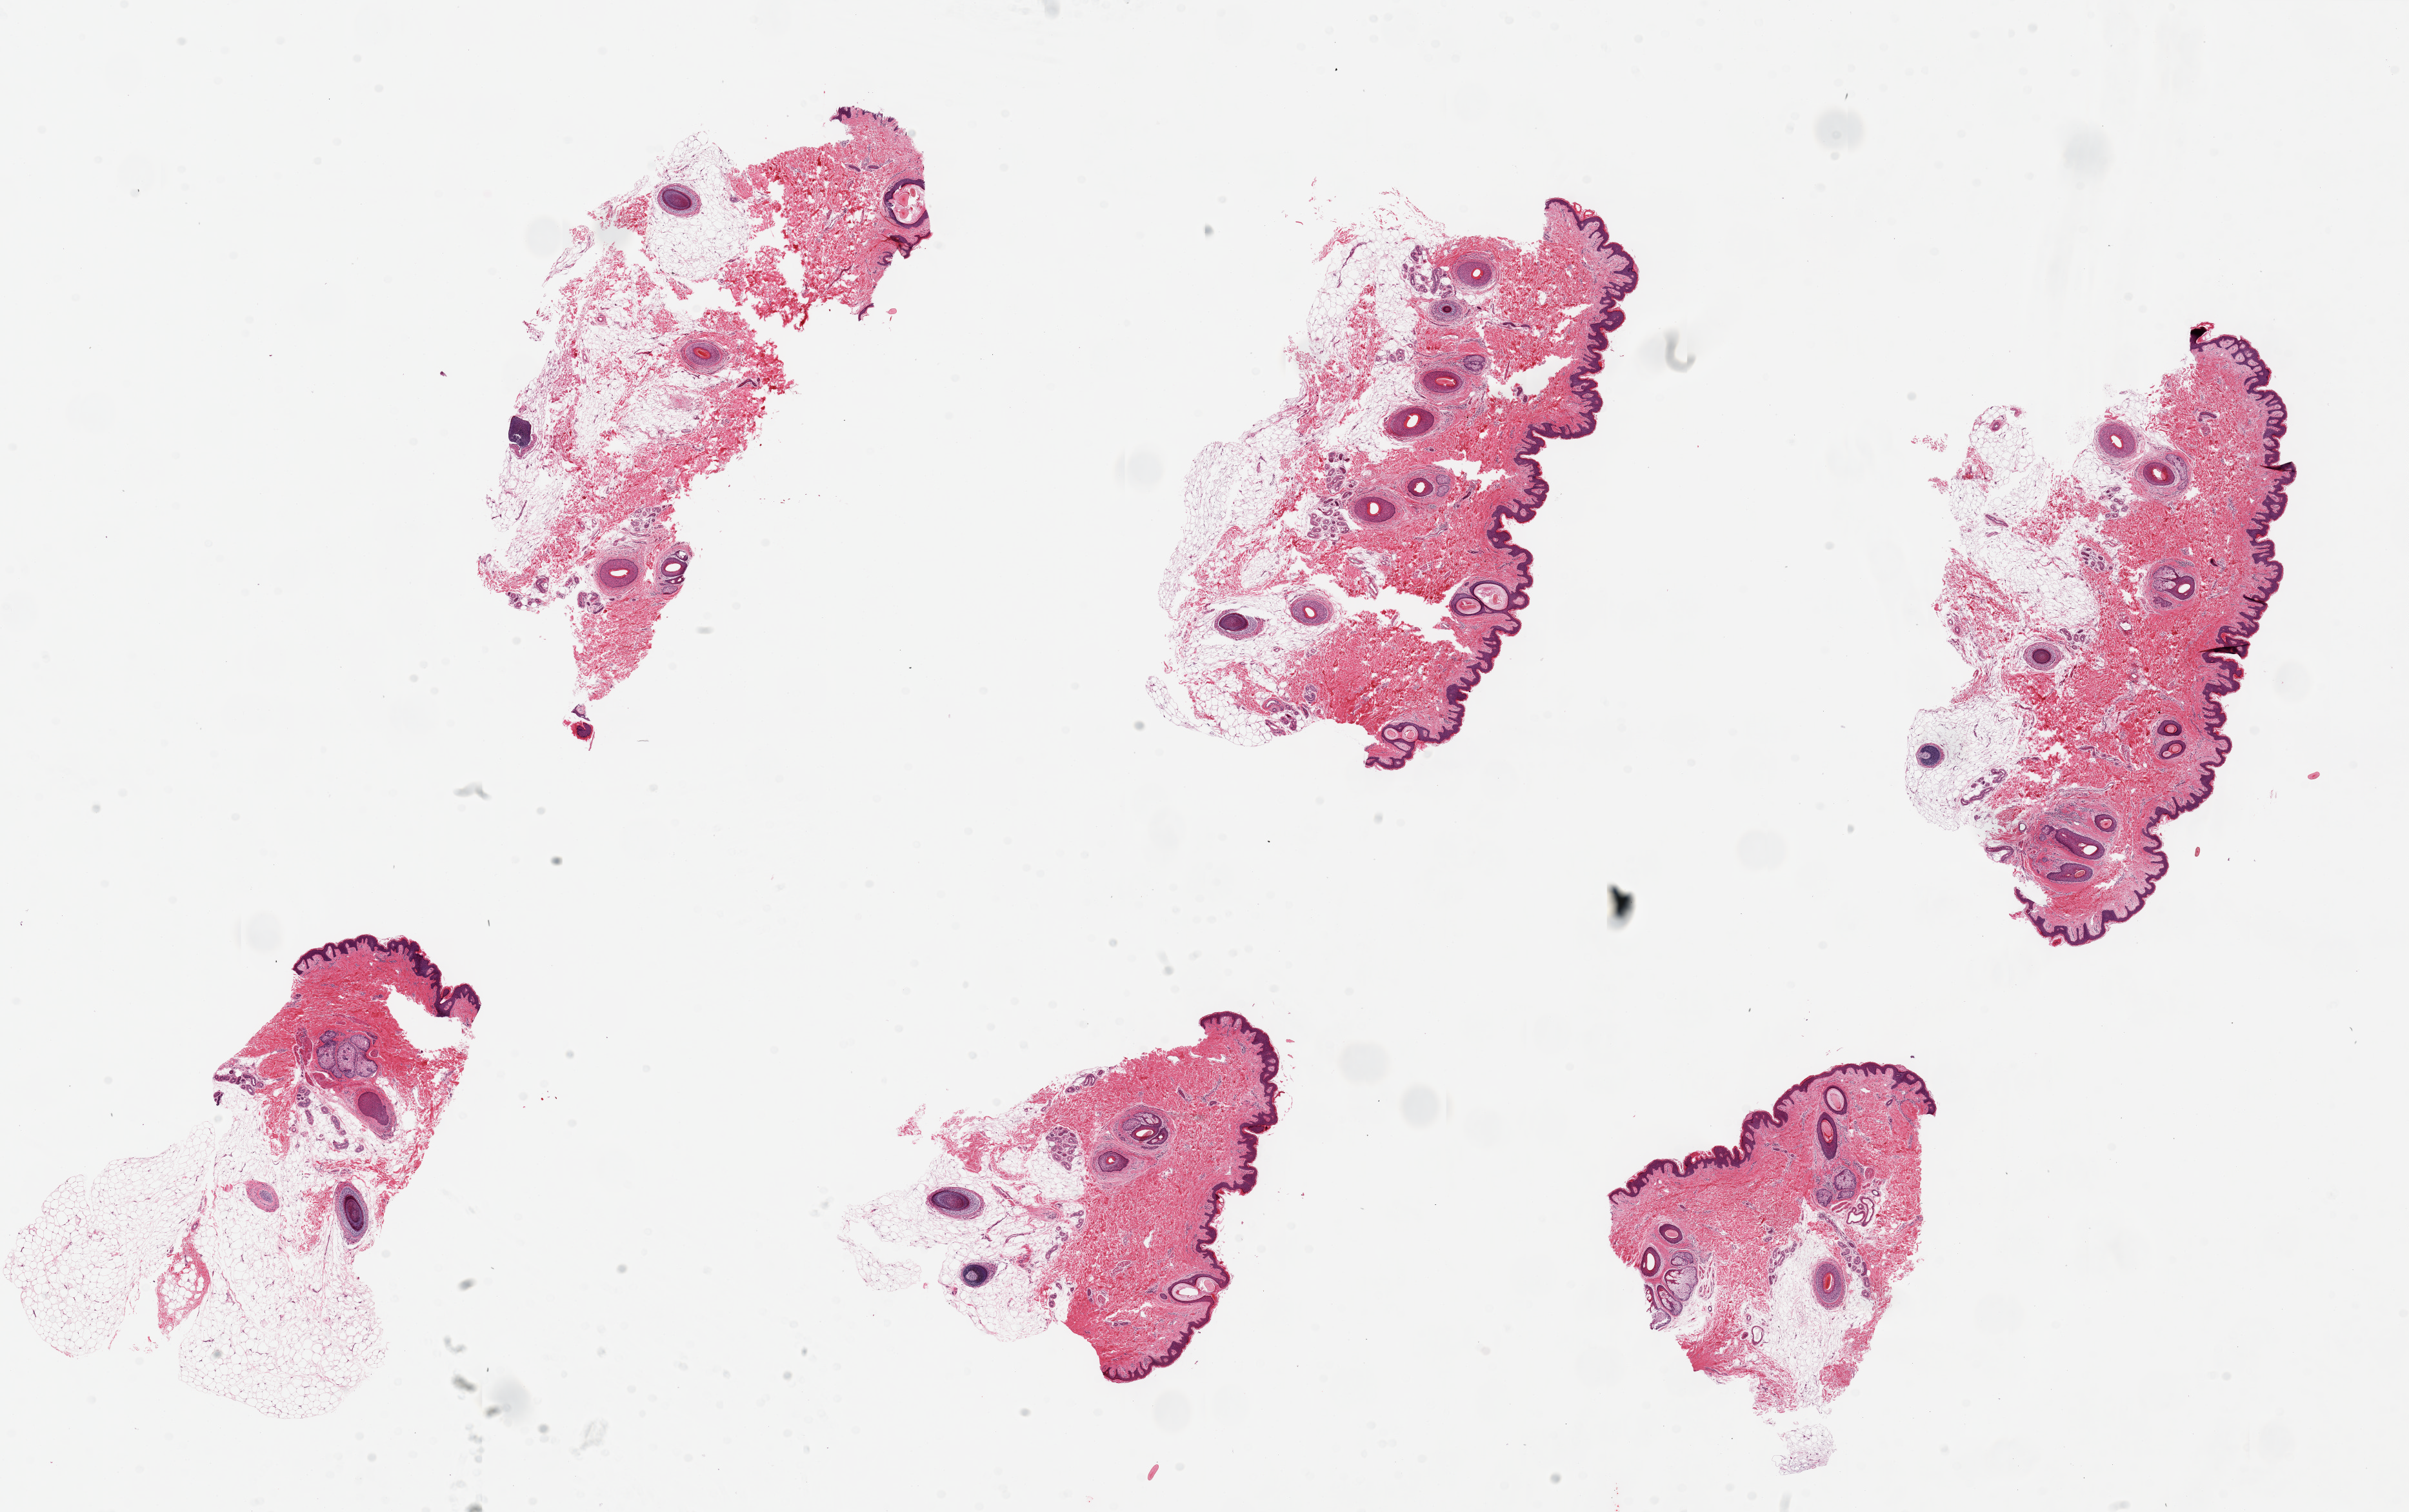
Hematoxylin and eosin (H&E) whole-slide image, brightfield, whole scanned area (about 29.5 x 18.5 mm) shown as a low-resolution overview; PAXgene-fixed paraffin-embedded (PFPE) section; sampled site (target tissue): skin of suprapubic region; donor tissue sample.
Reviewer comment on this tissue sample: 6 pieces ~8x2.5mm; Squamous epithelium is ~2-3% of thickness; abundant adnexal structures (hair, sebaceous glands, a few epidermal inclusion cysts) are present.